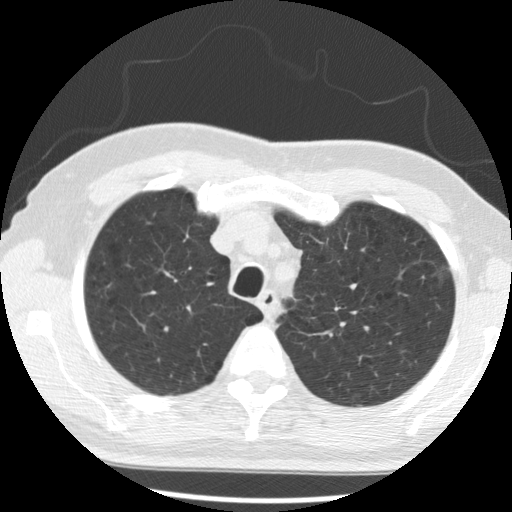
Axial slice from a low-dose chest CT screening exam. Second annual screen. Lung window (W 1500 / L -600 HU). 2.5 mm slice thickness. Standard (soft-tissue) reconstruction kernel (STANDARD). Slice 61 of 285 in the series. 512 × 512 image matrix. Male, age 68 years at enrolment. Current smoker at enrolment.
Expert-annotated lung lesion, bounding box [x1, y1, x2, y2] px = [419, 262, 460, 294]. The exam's reader record, not a measurement of the box and not confirmed to be the same lesion: non-calcified nodule or mass ≥4 mm, left upper lobe, 15 × 11 mm, poorly defined margins, ground glass attenuation, pre-existing on the prior screen: yes; interval growth: yes. Later outcome: lung cancer diagnosed 278 days after this screen — bronchiolo-alveolar adenocarcinoma, NOS, left upper lobe, moderately differentiated (G2), stage IA (AJCC 6th edition), 17 mm at pathology.